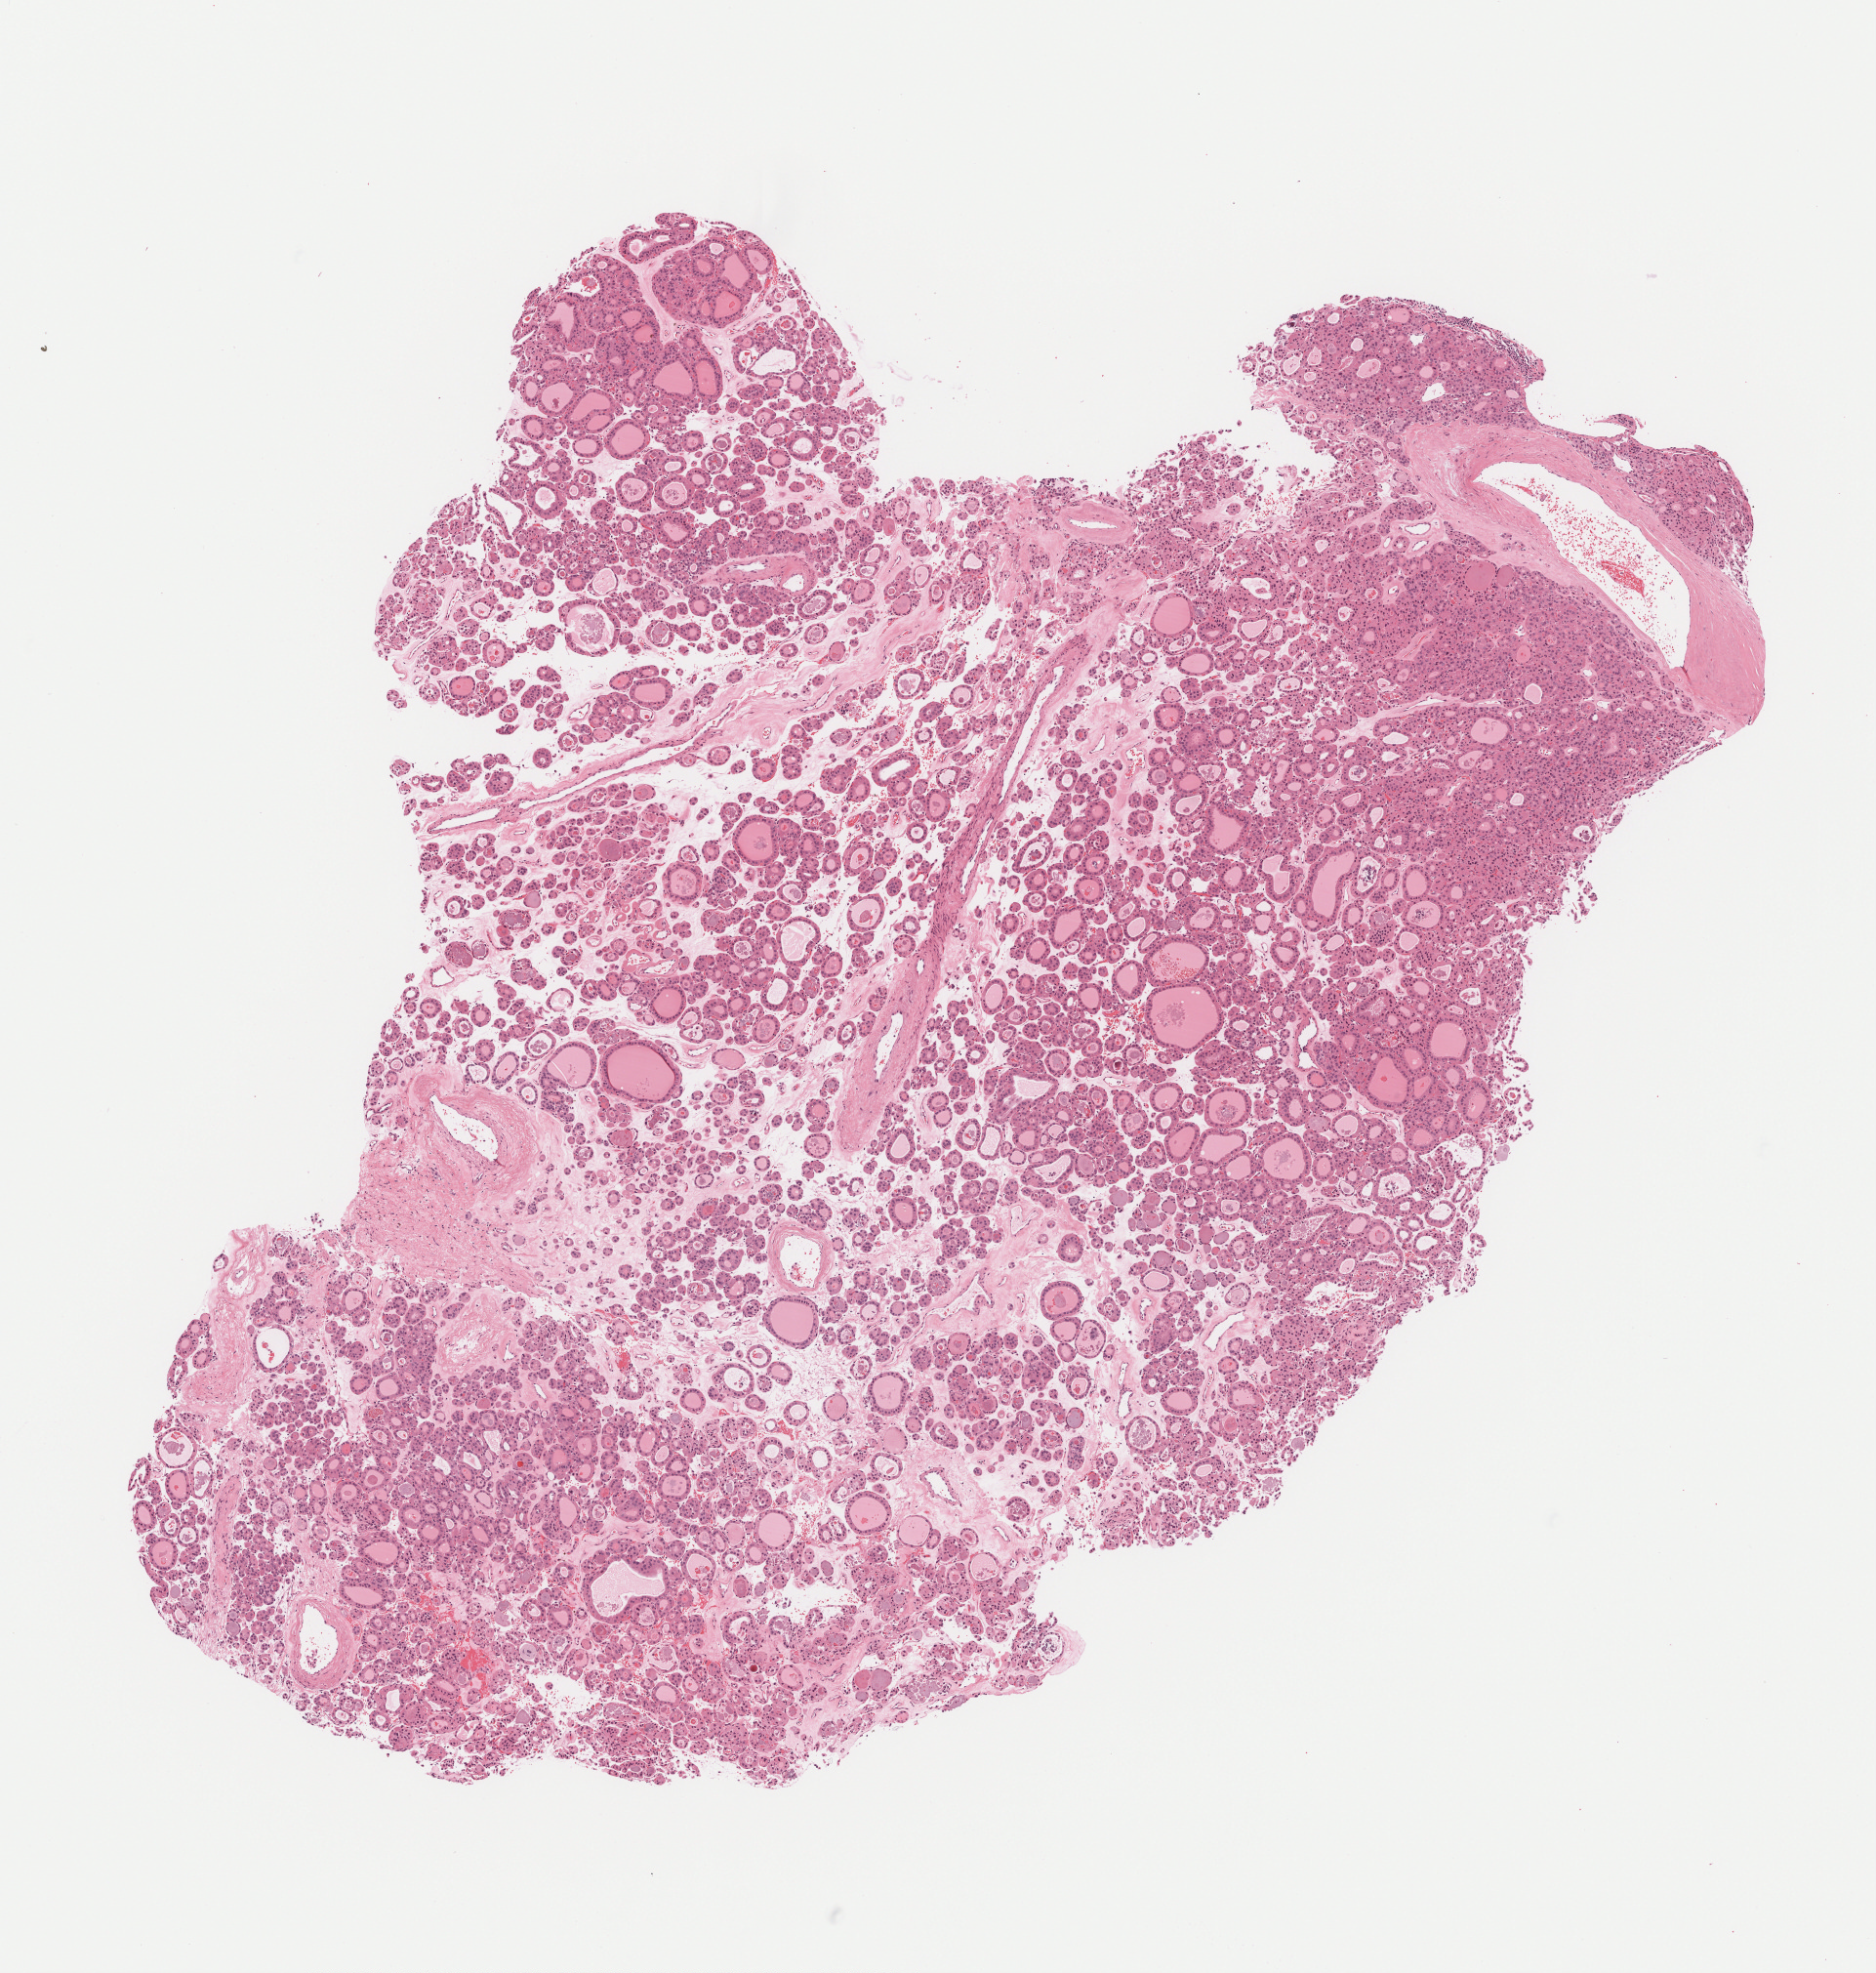
Hematoxylin and eosin (H&E) stained whole-slide image, low-resolution overview of the scanned area, about 7.7 x 8.1 mm, formalin-fixed paraffin-embedded (FFPE) diagnostic section, primary tumour sample from the thyroid. Female, age 68 years at initial diagnosis.
AJCC pathologic stage: I. Histologic diagnosis: Papillary carcinoma, follicular variant (thyroid gland). Lymph nodes positive (case pathology): 0 of 2 examined. Laterality: right.